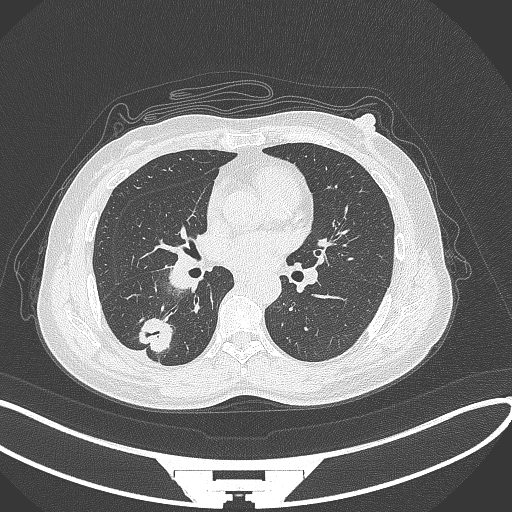
Chest CT, one axial slice. Position 149 of 352 along the scan axis. Reconstruction kernel B70f. Lung window (W 1500 / L -600 HU). 1 mm slice thickness. 512 × 512 image matrix. Female patient, age 55 years. Case-level facts recorded for this patient, not image findings: clinical TNM (as recorded): T1c N1 M0.
Annotated regions visible in this slice (bounding box drawn by a radiologist):
- lung tumour (recorded histology: adenocarcinoma): bounding box [x1, y1, x2, y2] px = [136, 311, 177, 356]